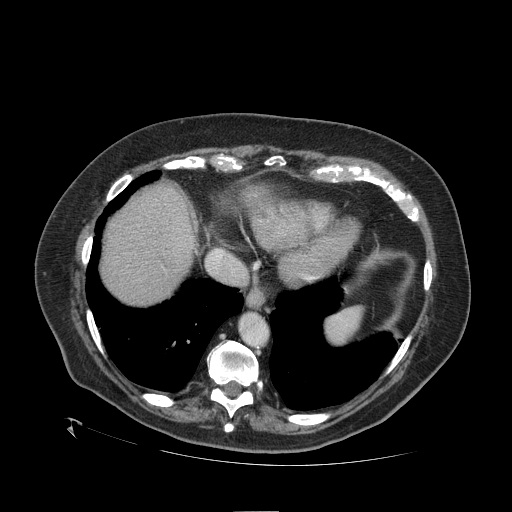
Contrast-enhanced abdominal CT (liver protocol), one axial slice; position 94 of 109 along the scan axis; one of 2 acquisitions stored at this slice position; soft-tissue window (W 400 / L 40 HU); 512 × 512 image matrix. Case-level facts recorded for this patient, not image findings: diagnosis: hepatocellular carcinoma (patient treated with transarterial chemoembolisation; whether this scan precedes or follows treatment is not stated here); TNM stage (as recorded): Stage-I; Child-Pugh class: A; tumour nodularity: uninodular; tumour size: 4.6 cm.
Outlined on this slice (semi-automatic segmentation, software-assisted and operator-edited):
- abdominal aorta: bounding box (x1, y1, x2, y2) in pixels: (241, 314, 267, 345)
- liver parenchyma outside the tumour (the mass and vessels are separate outlines, so this box may not span the whole liver): (102, 184, 195, 304)